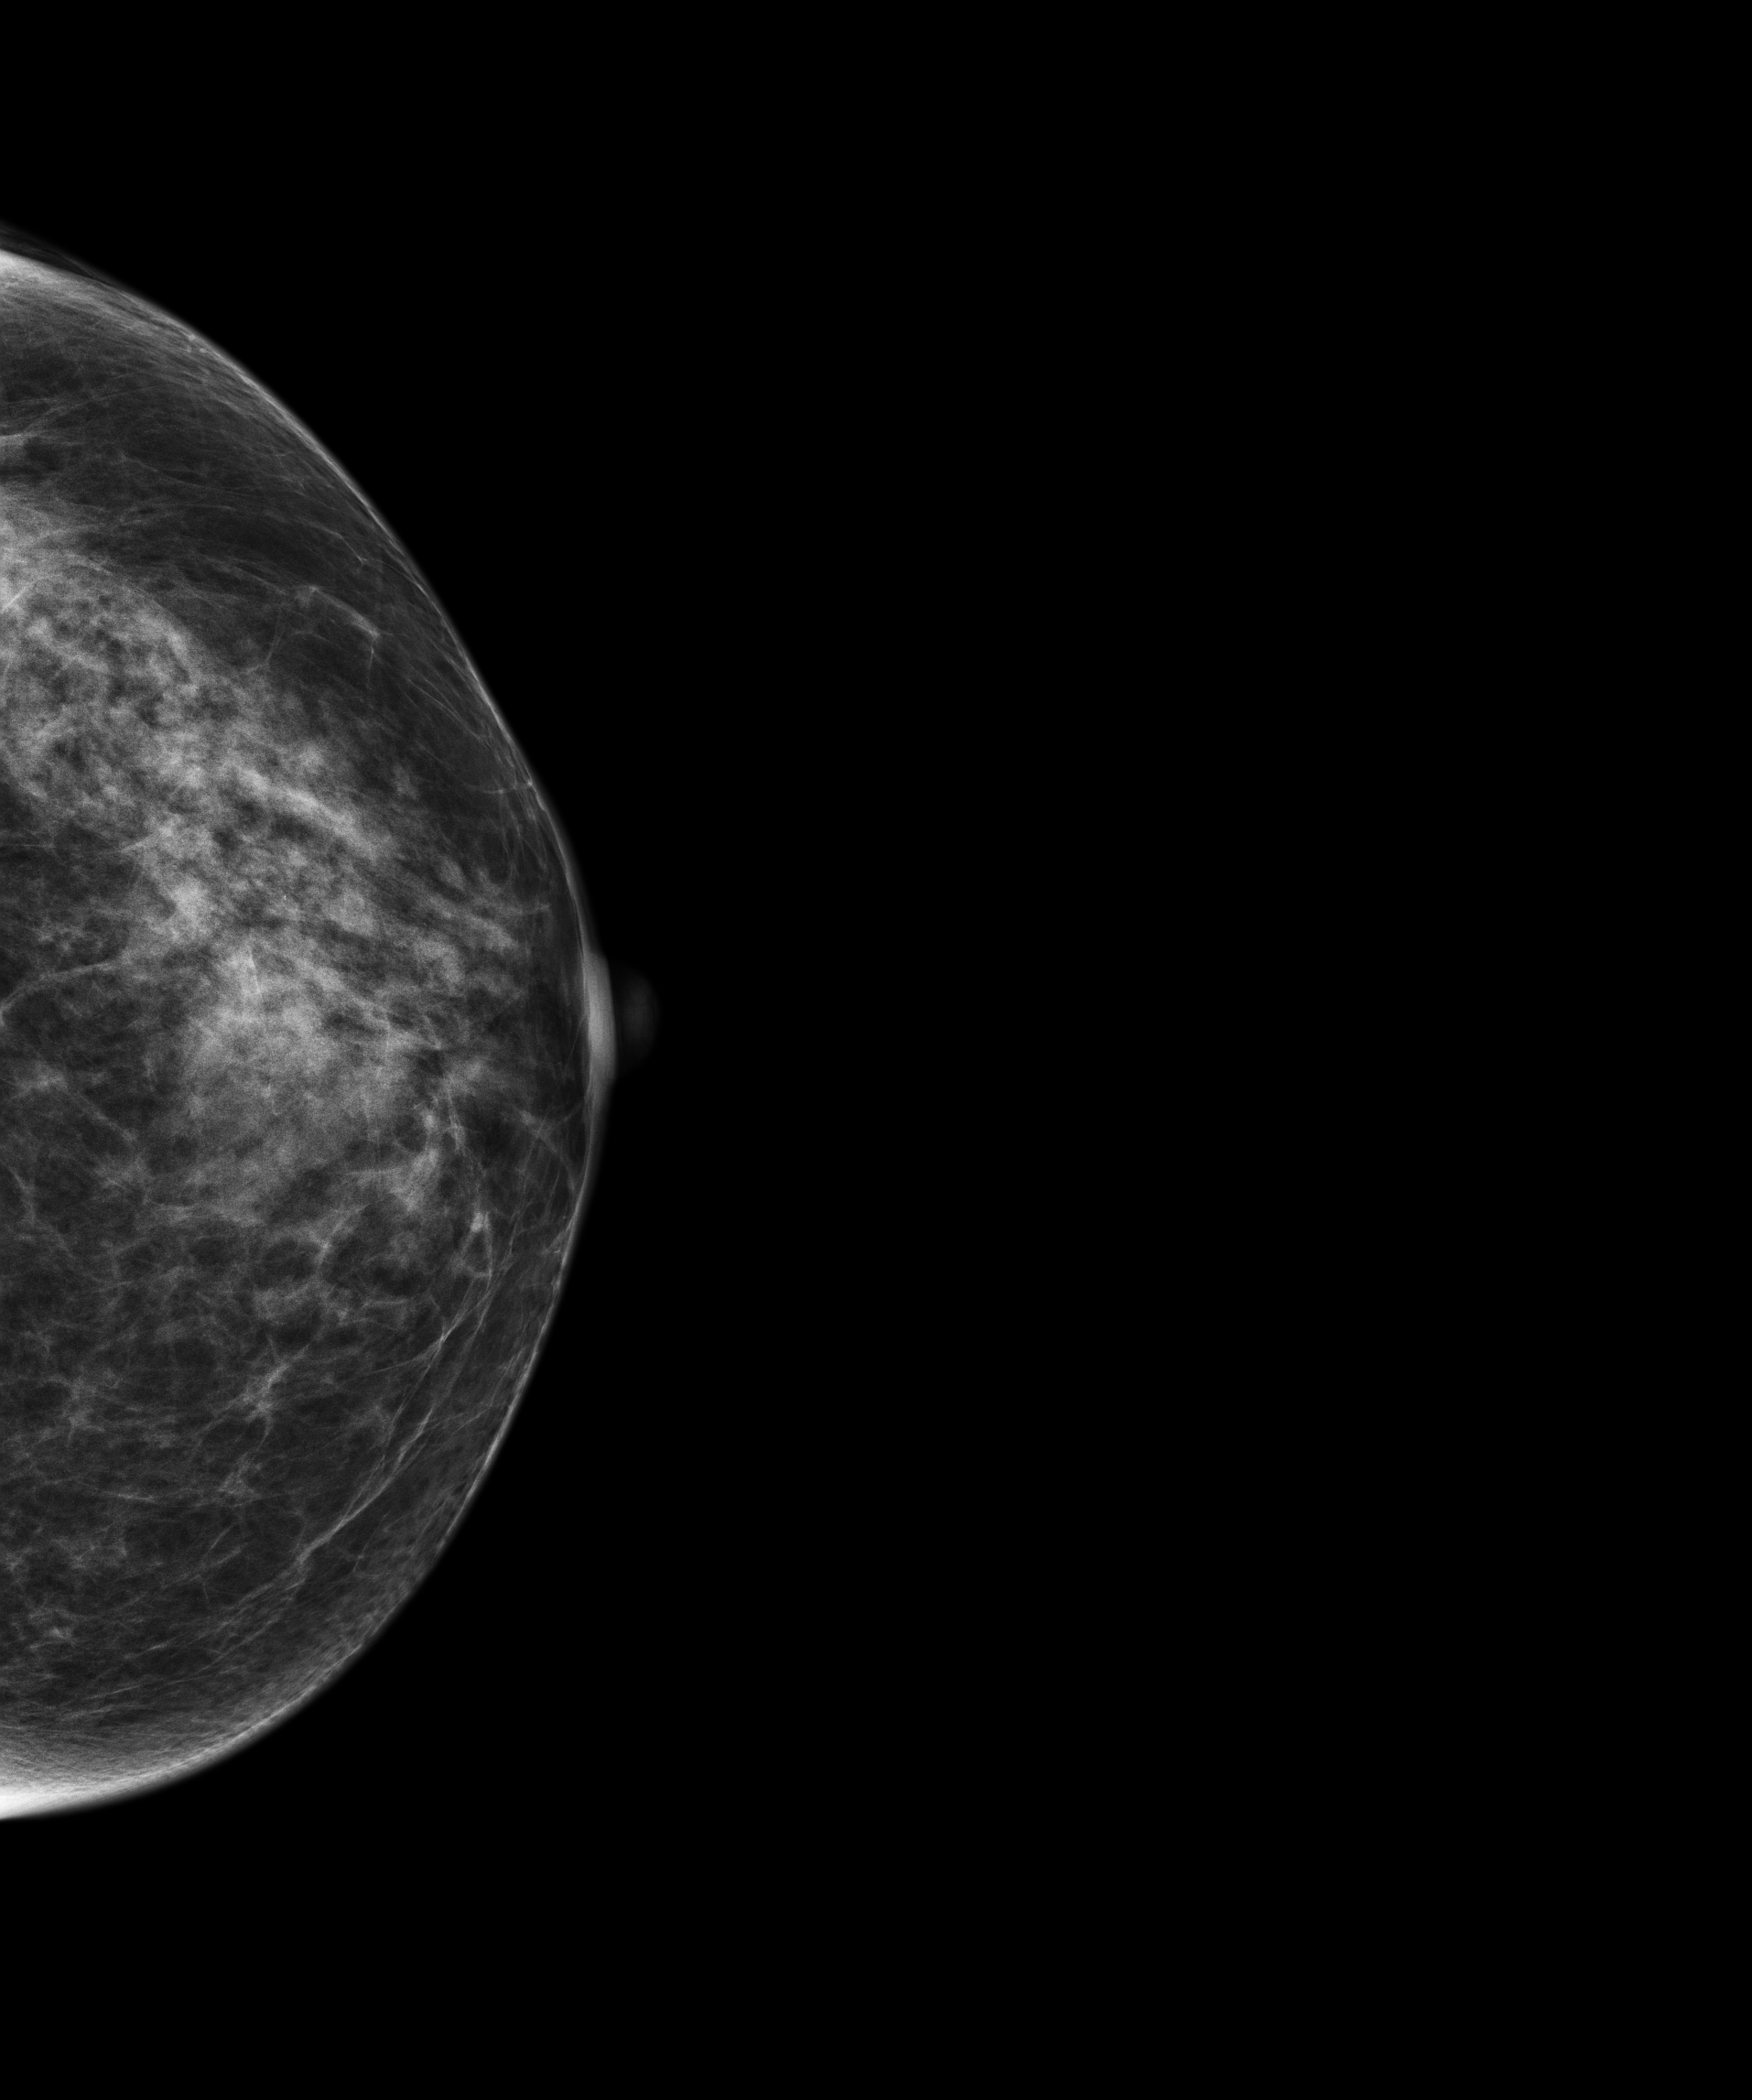
Full-field digital mammogram (FFDM); left breast; craniocaudal (CC) view; annual screening mammography examination; system: Senographe Essential ADS_56.21.3. Patient aged 61 years (female).
BI-RADS breast density category at the screening exam (both breasts, scale 1–4): 3. Final BI-RADS assessment for this screening round (tomosynthesis exam, both breasts): category 1. Recall: no recall after this screen.